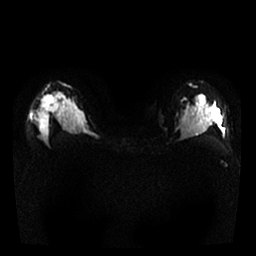
Breast MRI, one axial slice. Diffusion-weighted series; image 2 of 4 stored at this slice position (different b-values; order by instance number). 1.5 T. 256 × 256 image matrix. Female patient.
Annotated regions visible in this slice (outlined manually by an expert reader):
- tumour on diffusion-weighted imaging: bounding box [x1, y1, x2, y2] px = [43, 95, 59, 112]